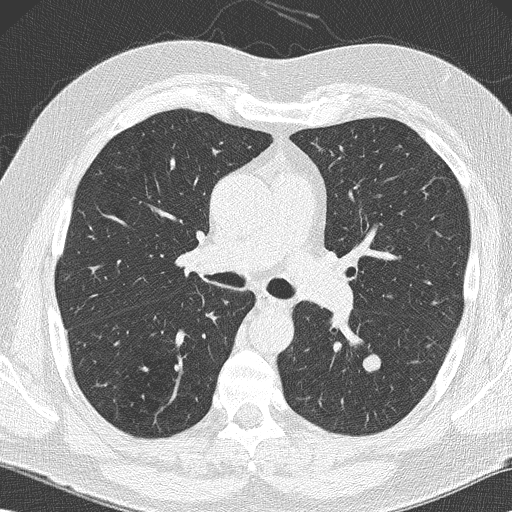
Low-dose screening chest CT, axial slice, baseline screening round, lung window (W 1500 / L -600 HU), slice 66 of 152 in the series, 512 × 512 image matrix, field of view 350 × 350 mm. Male participant, aged 59 years at enrolment.
Expert-annotated lung lesion, box from (x=347, y=348) to (x=390, y=384) px. The screening reader recorded 2 non-calcified nodules or masses ≥4 mm on this exam; which of them this box marks is not recorded. Later outcome: lung cancer diagnosed 61 days after this screen — large cell carcinoma, NOS, left lower lobe, poorly differentiated (G3), stage IA (AJCC 6th edition), 14 mm at pathology.